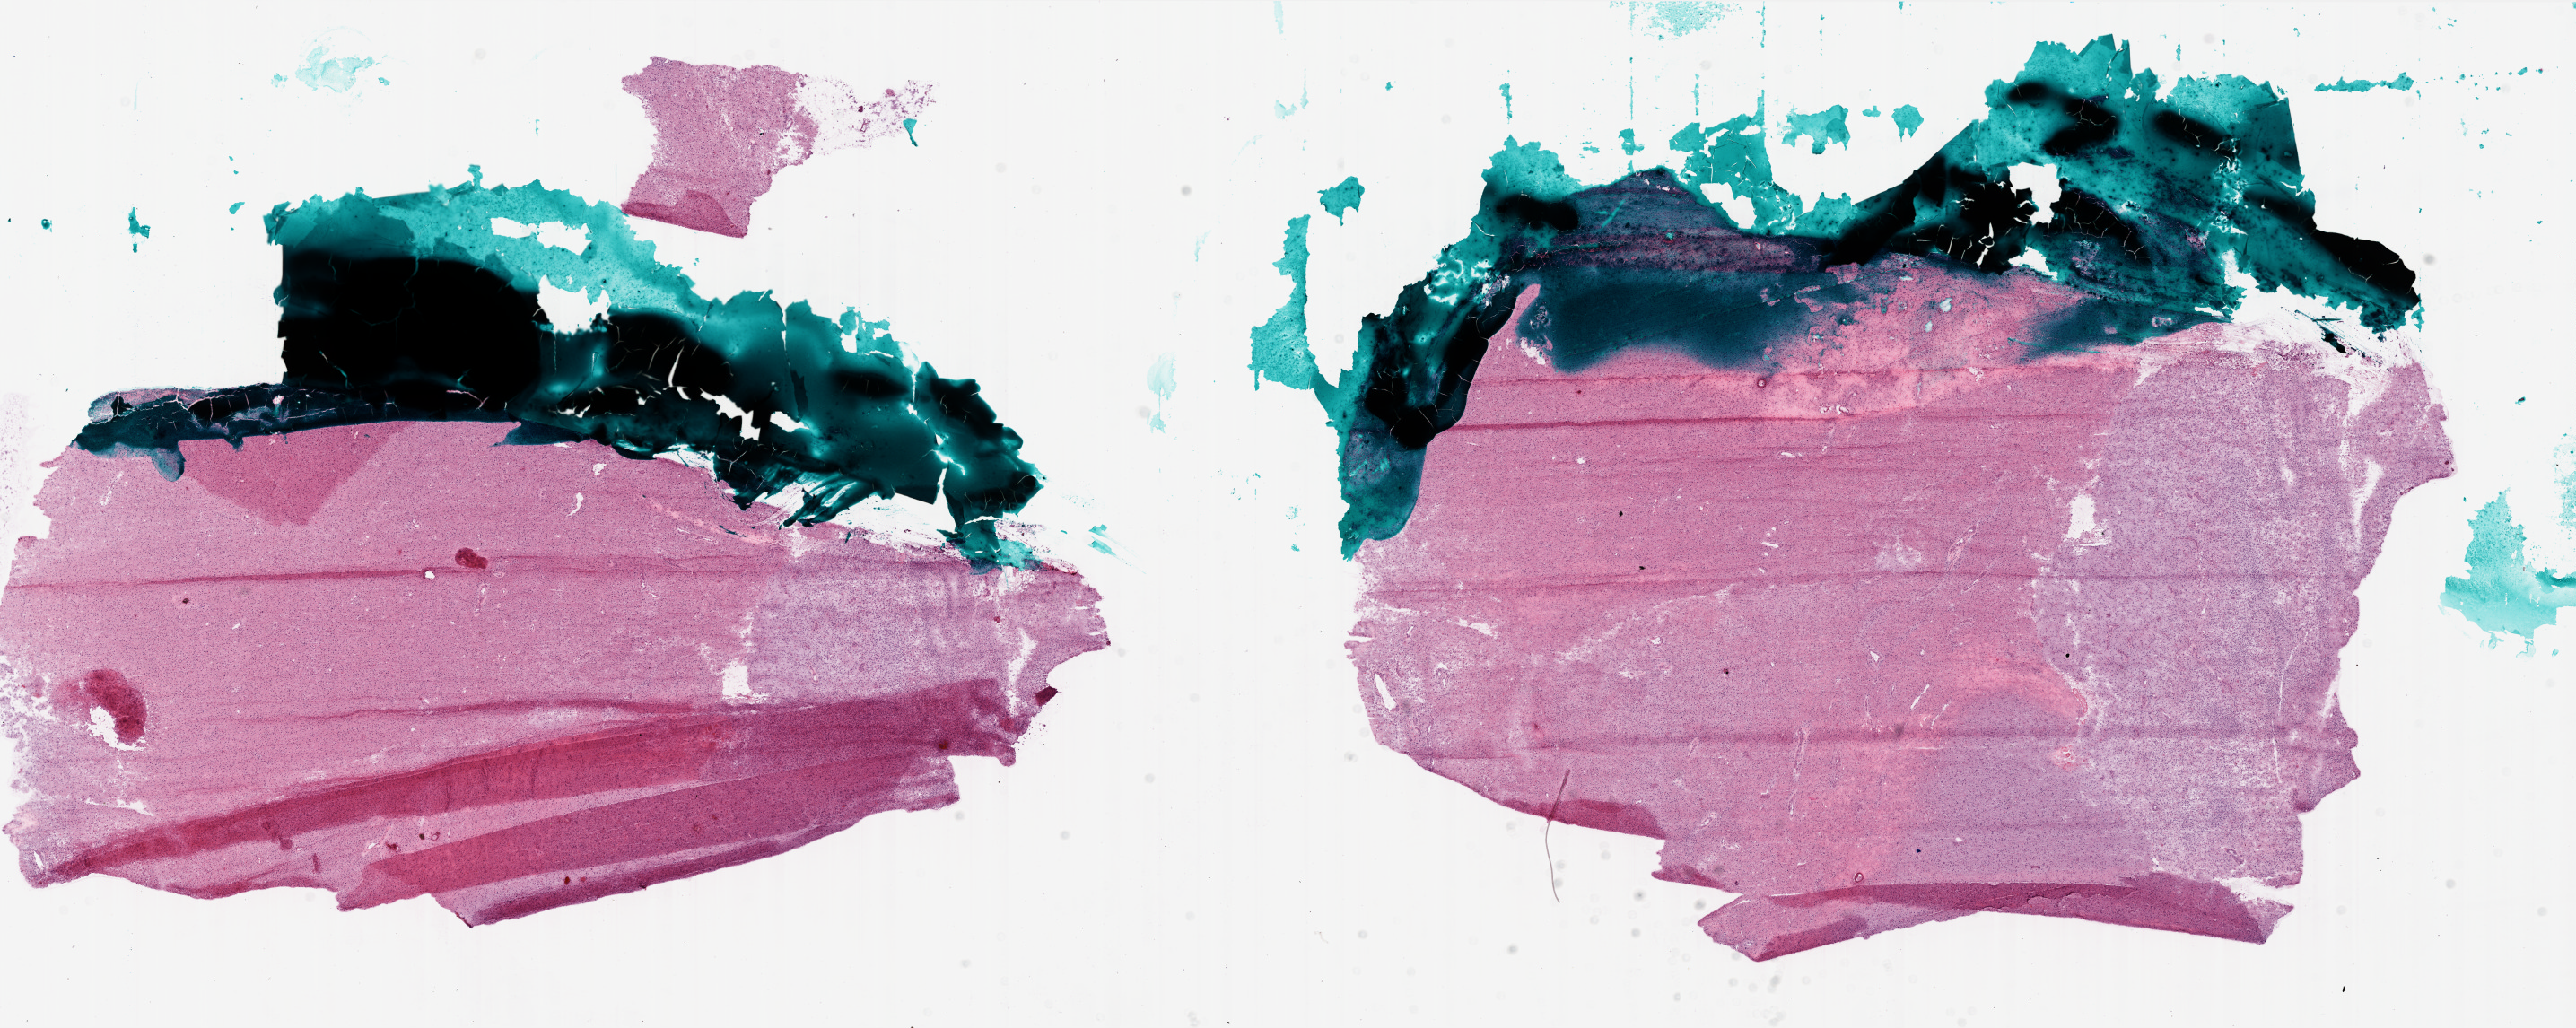
Whole-slide histology image, H&E-stained — whole scanned area (about 23.0 x 9.2 mm) shown as a low-resolution overview, frozen section from the bottom of the tissue portion, primary tumour sample from the brain. Patient: male, age at initial diagnosis 66 years. Slide review estimates, as recorded: tumour cells 25%, tumour nuclei 90%, normal cells 0%, stromal cells 70%, necrosis 5%.
Pathologic diagnosis: Glioblastoma.